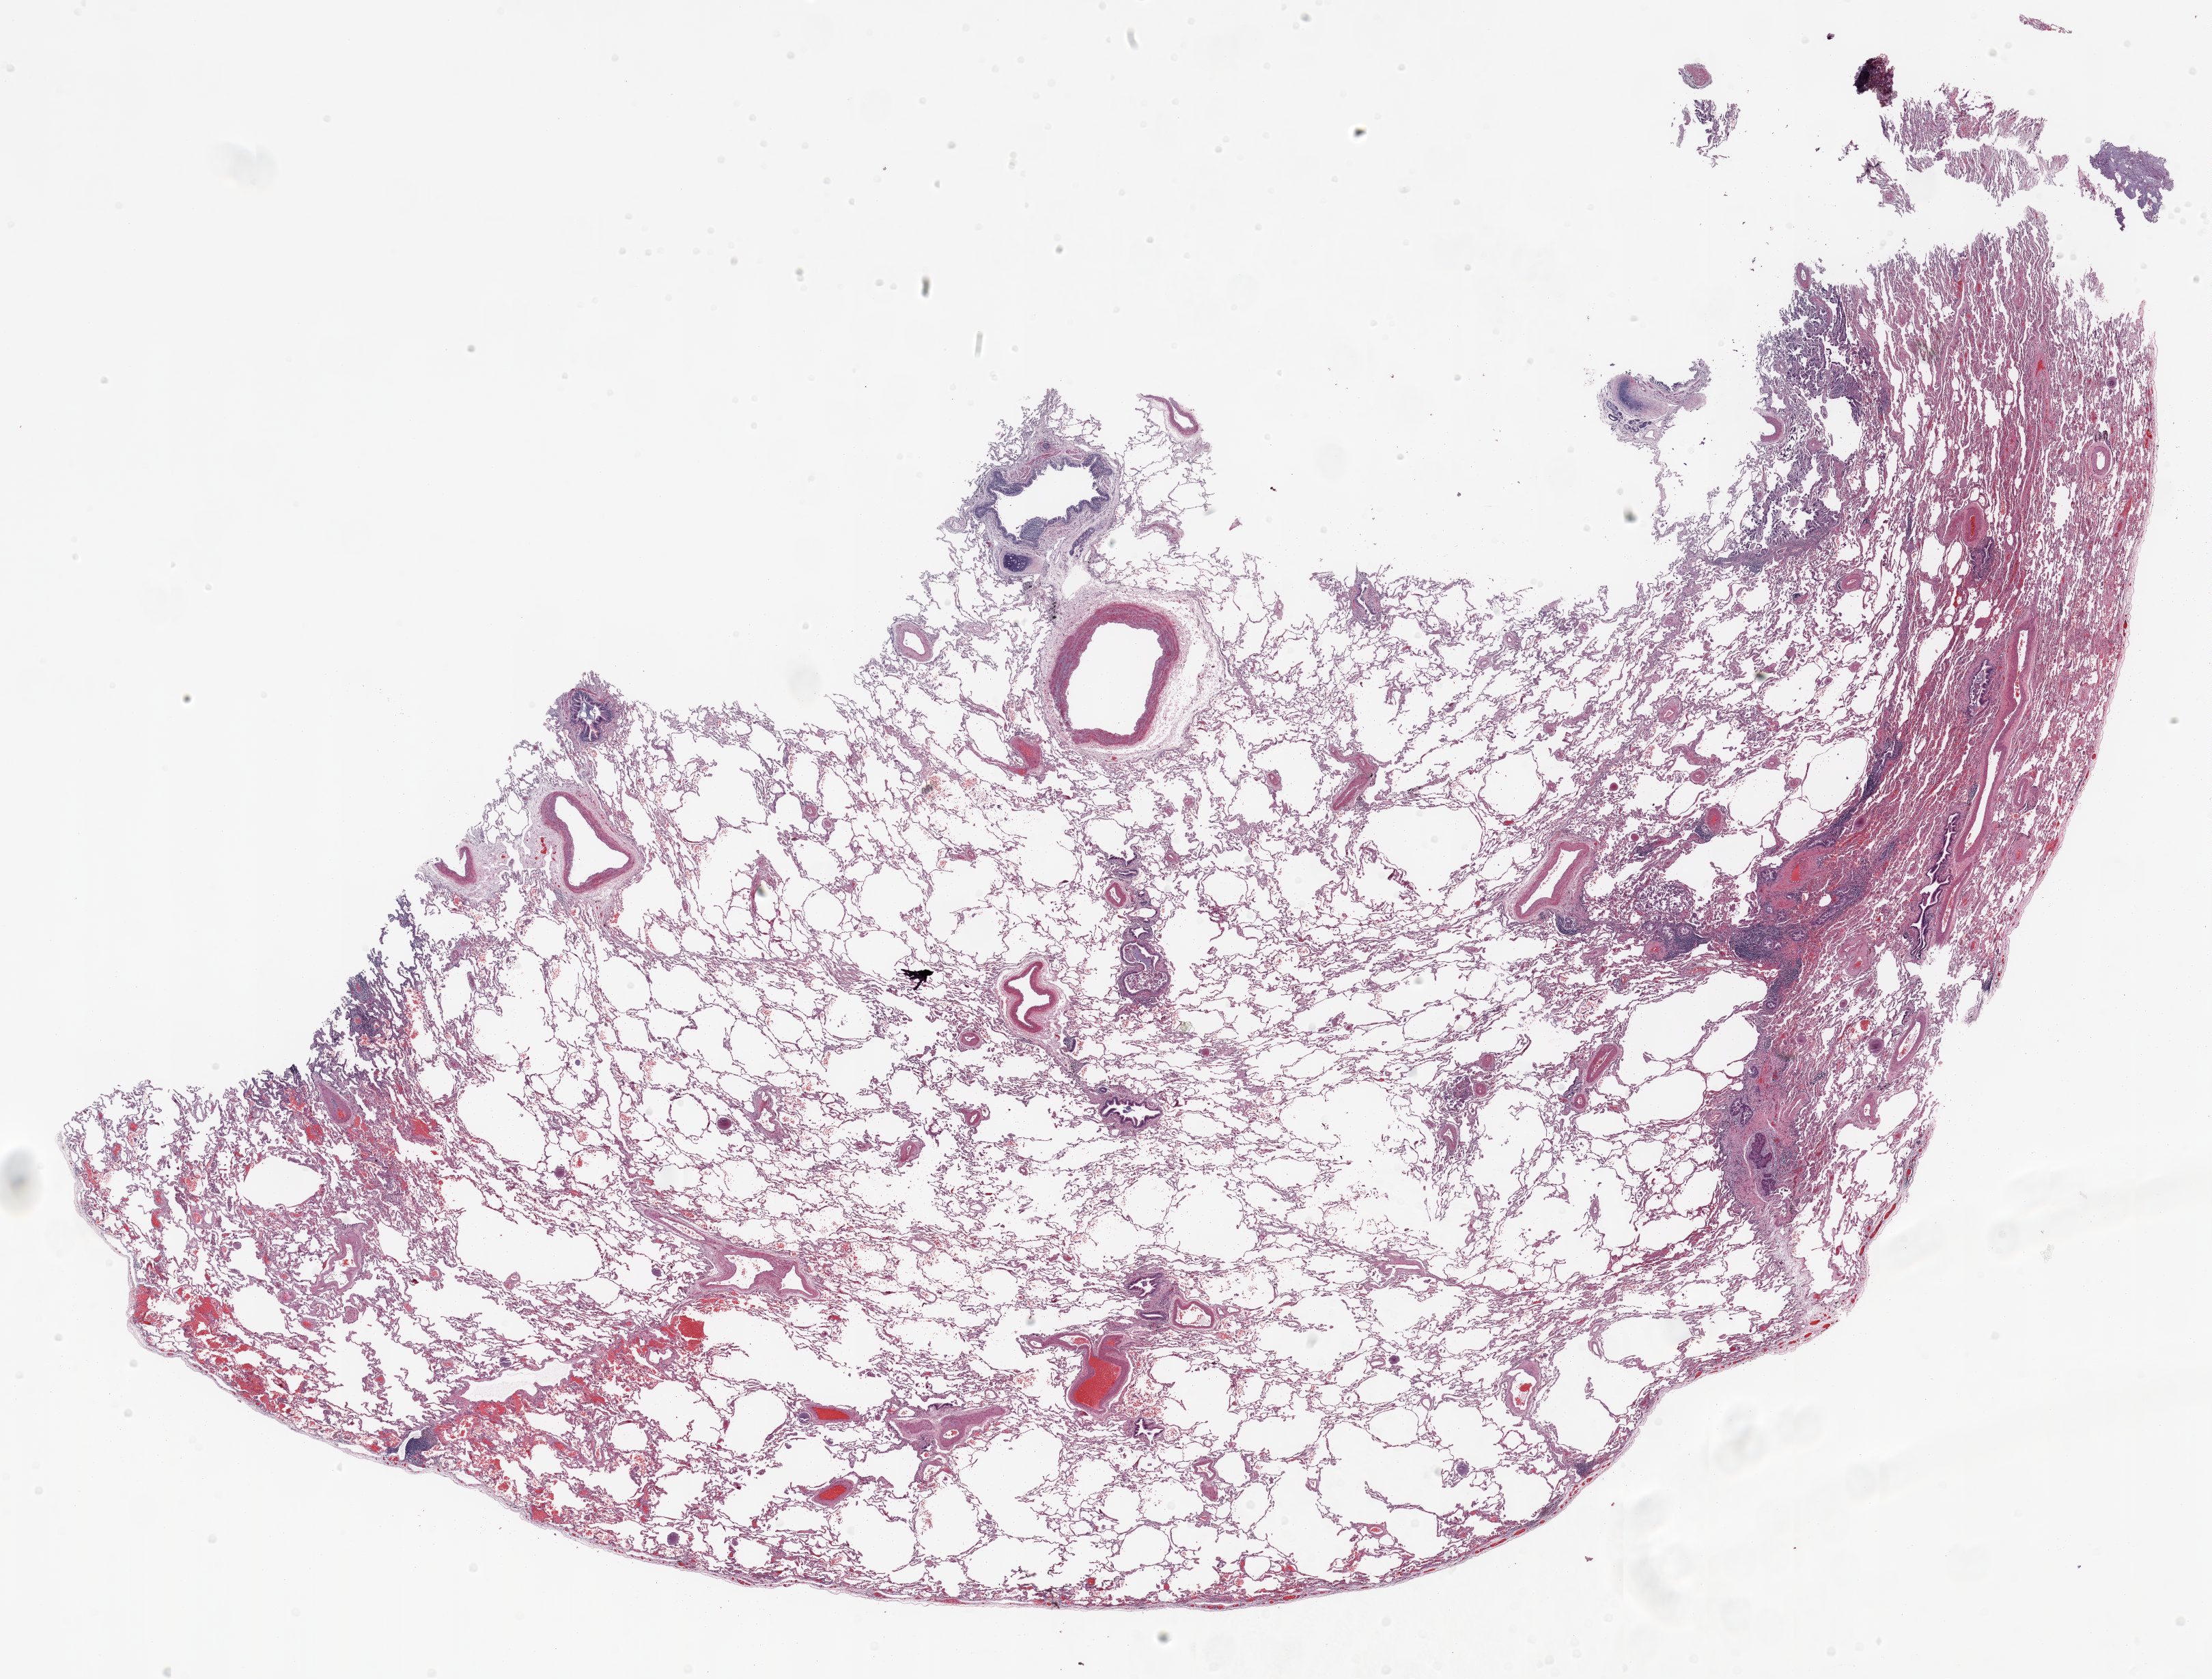
Whole-slide histology image, H&E-stained — whole scanned area (about 26.0 x 19.8 mm) shown as a low-resolution overview; formalin-fixed paraffin-embedded (FFPE) section; lung tissue. Female patient, aged 73 at enrolment. Current smoker at enrolment. Grade: moderately differentiated (G2).
Stage (AJCC 6th edition): IIIB. Tumour size (pathology): 12 mm. ICD-O-3 topography: upper lobe of lung (C34.1). Primary tumour location (clinical record): left upper lobe. Participant's lung-cancer diagnosis: Adenocarcinoma, NOS.